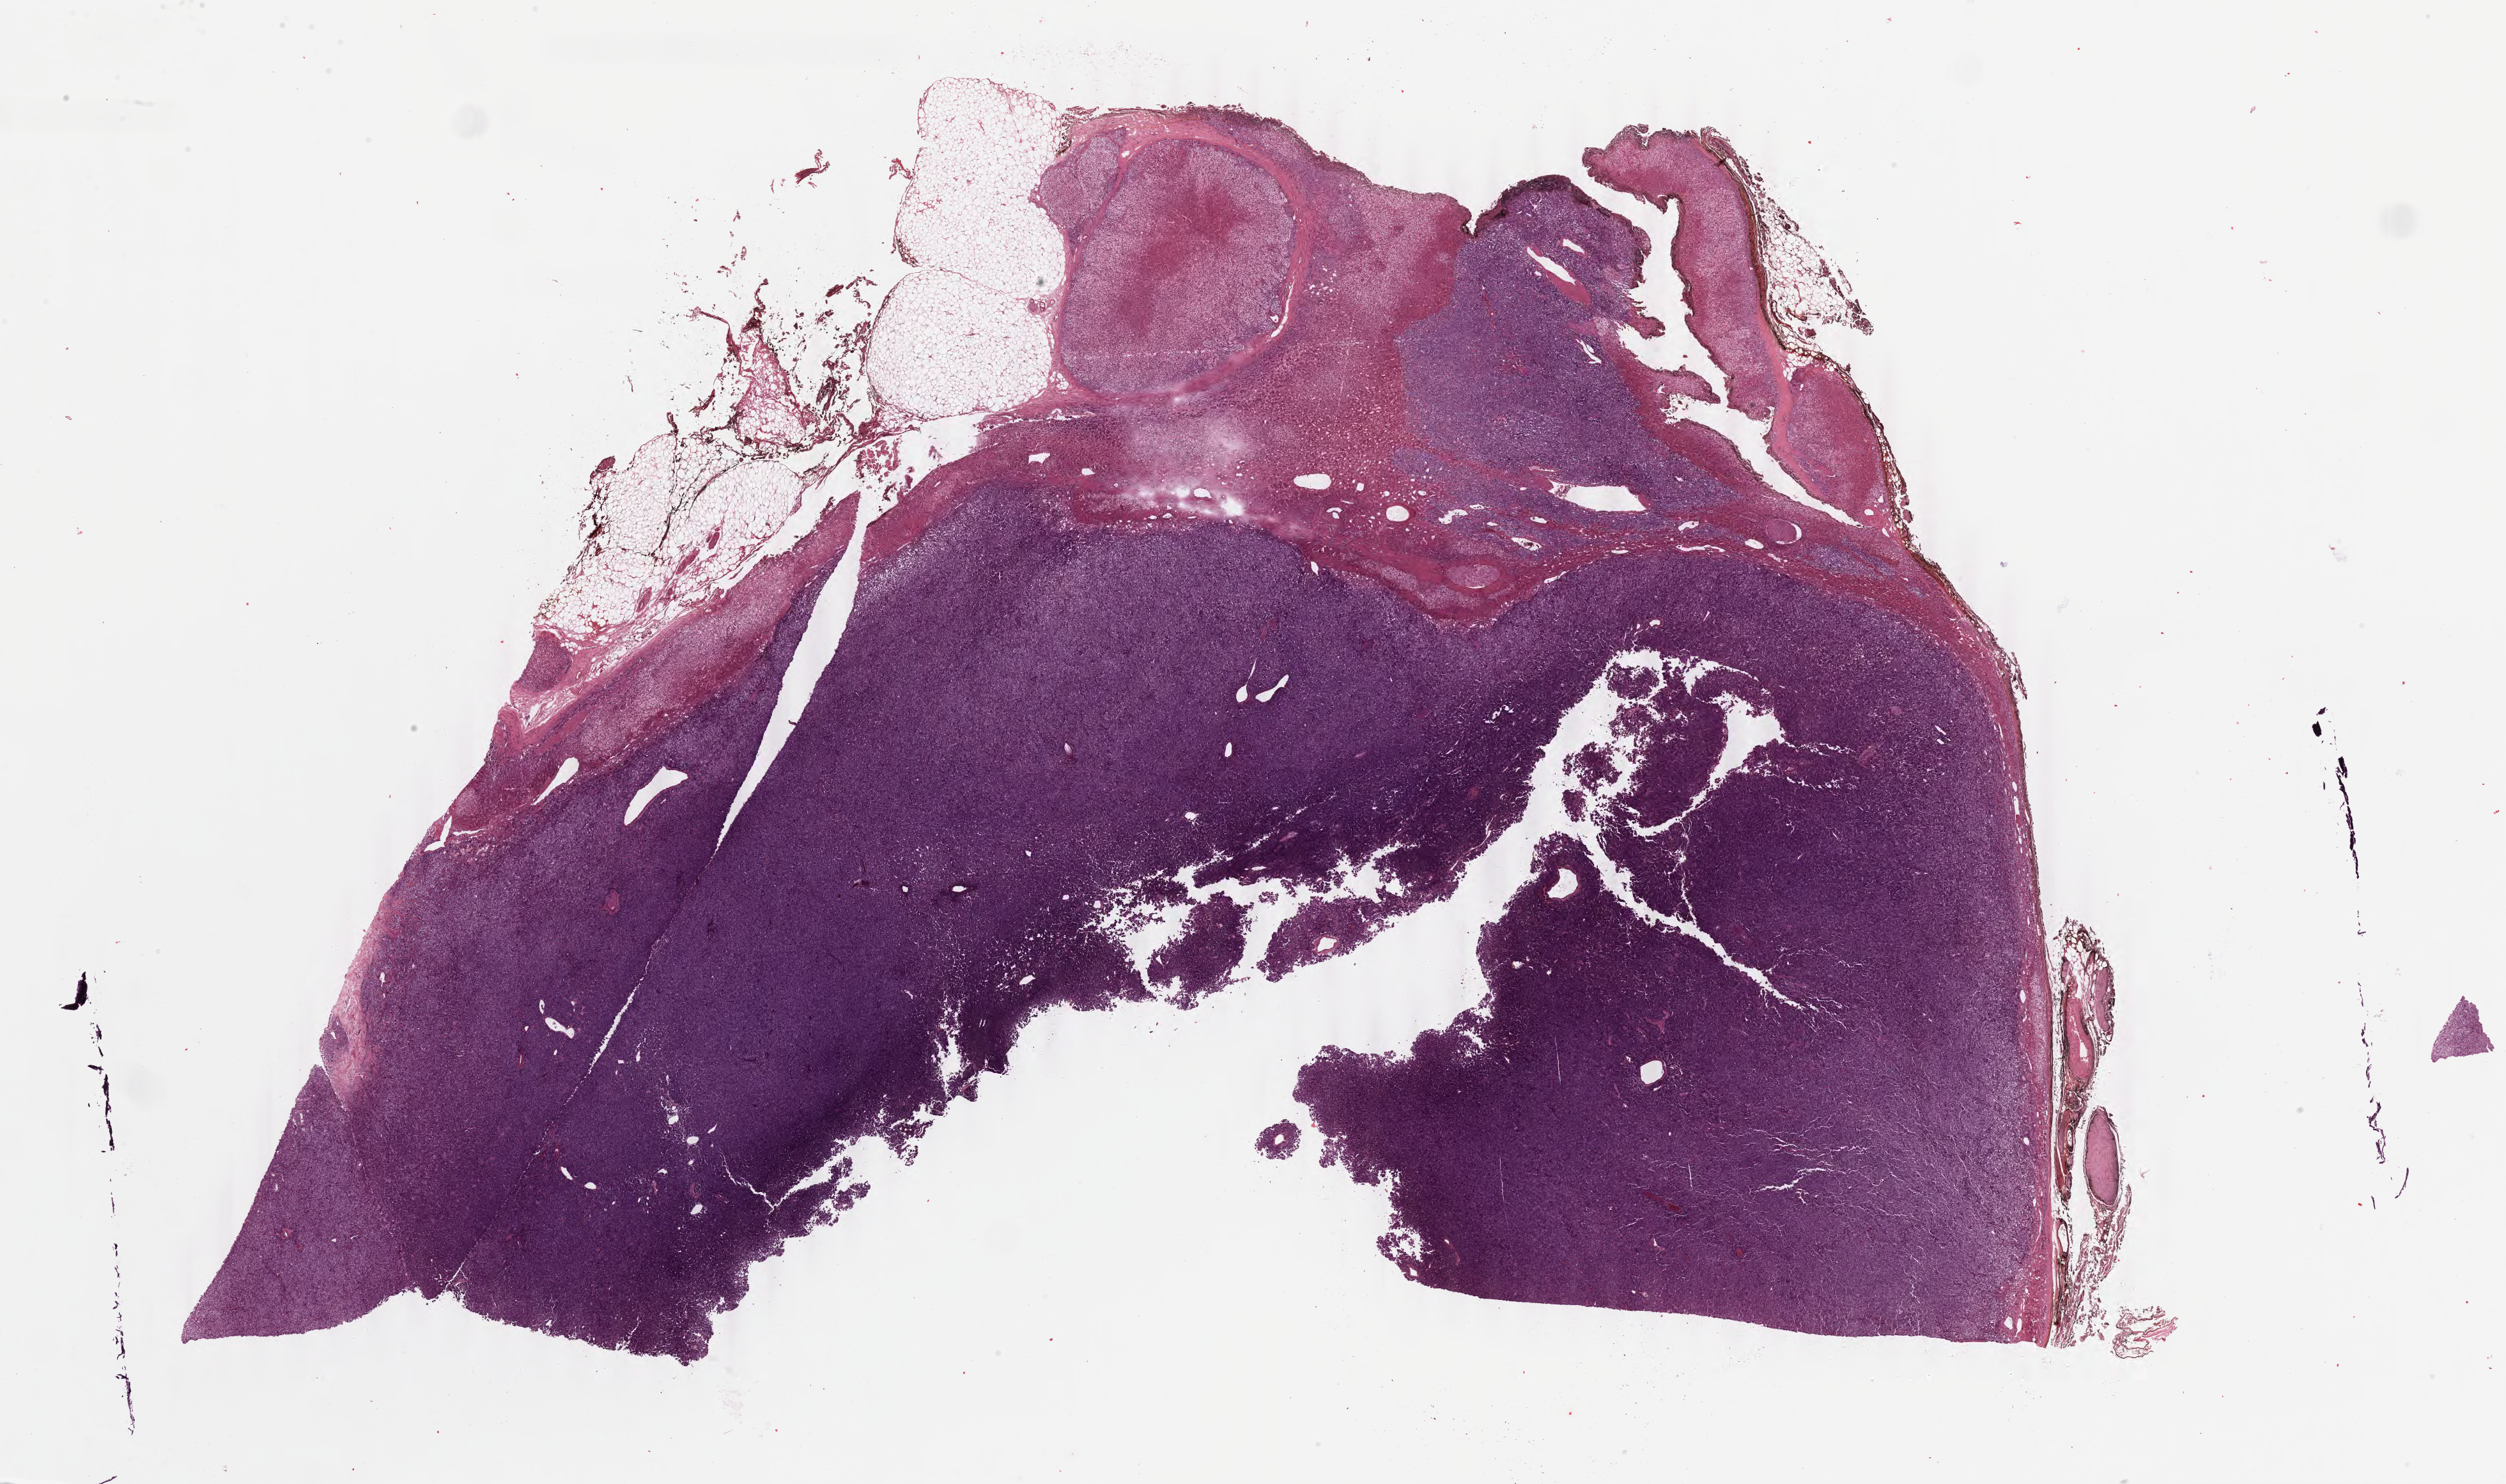
Whole-slide histology image, Hematoxylin and eosin (H&E) stained — a low-resolution overview of the entire scanned area, about 31.0 x 18.3 mm (acquisition: 40x scan); FFPE section; sample: primary tumour, adrenal gland. Male patient; age at initial diagnosis 47 years.
- laterality: right
- pathologic diagnosis: Pheochromocytoma, NOS